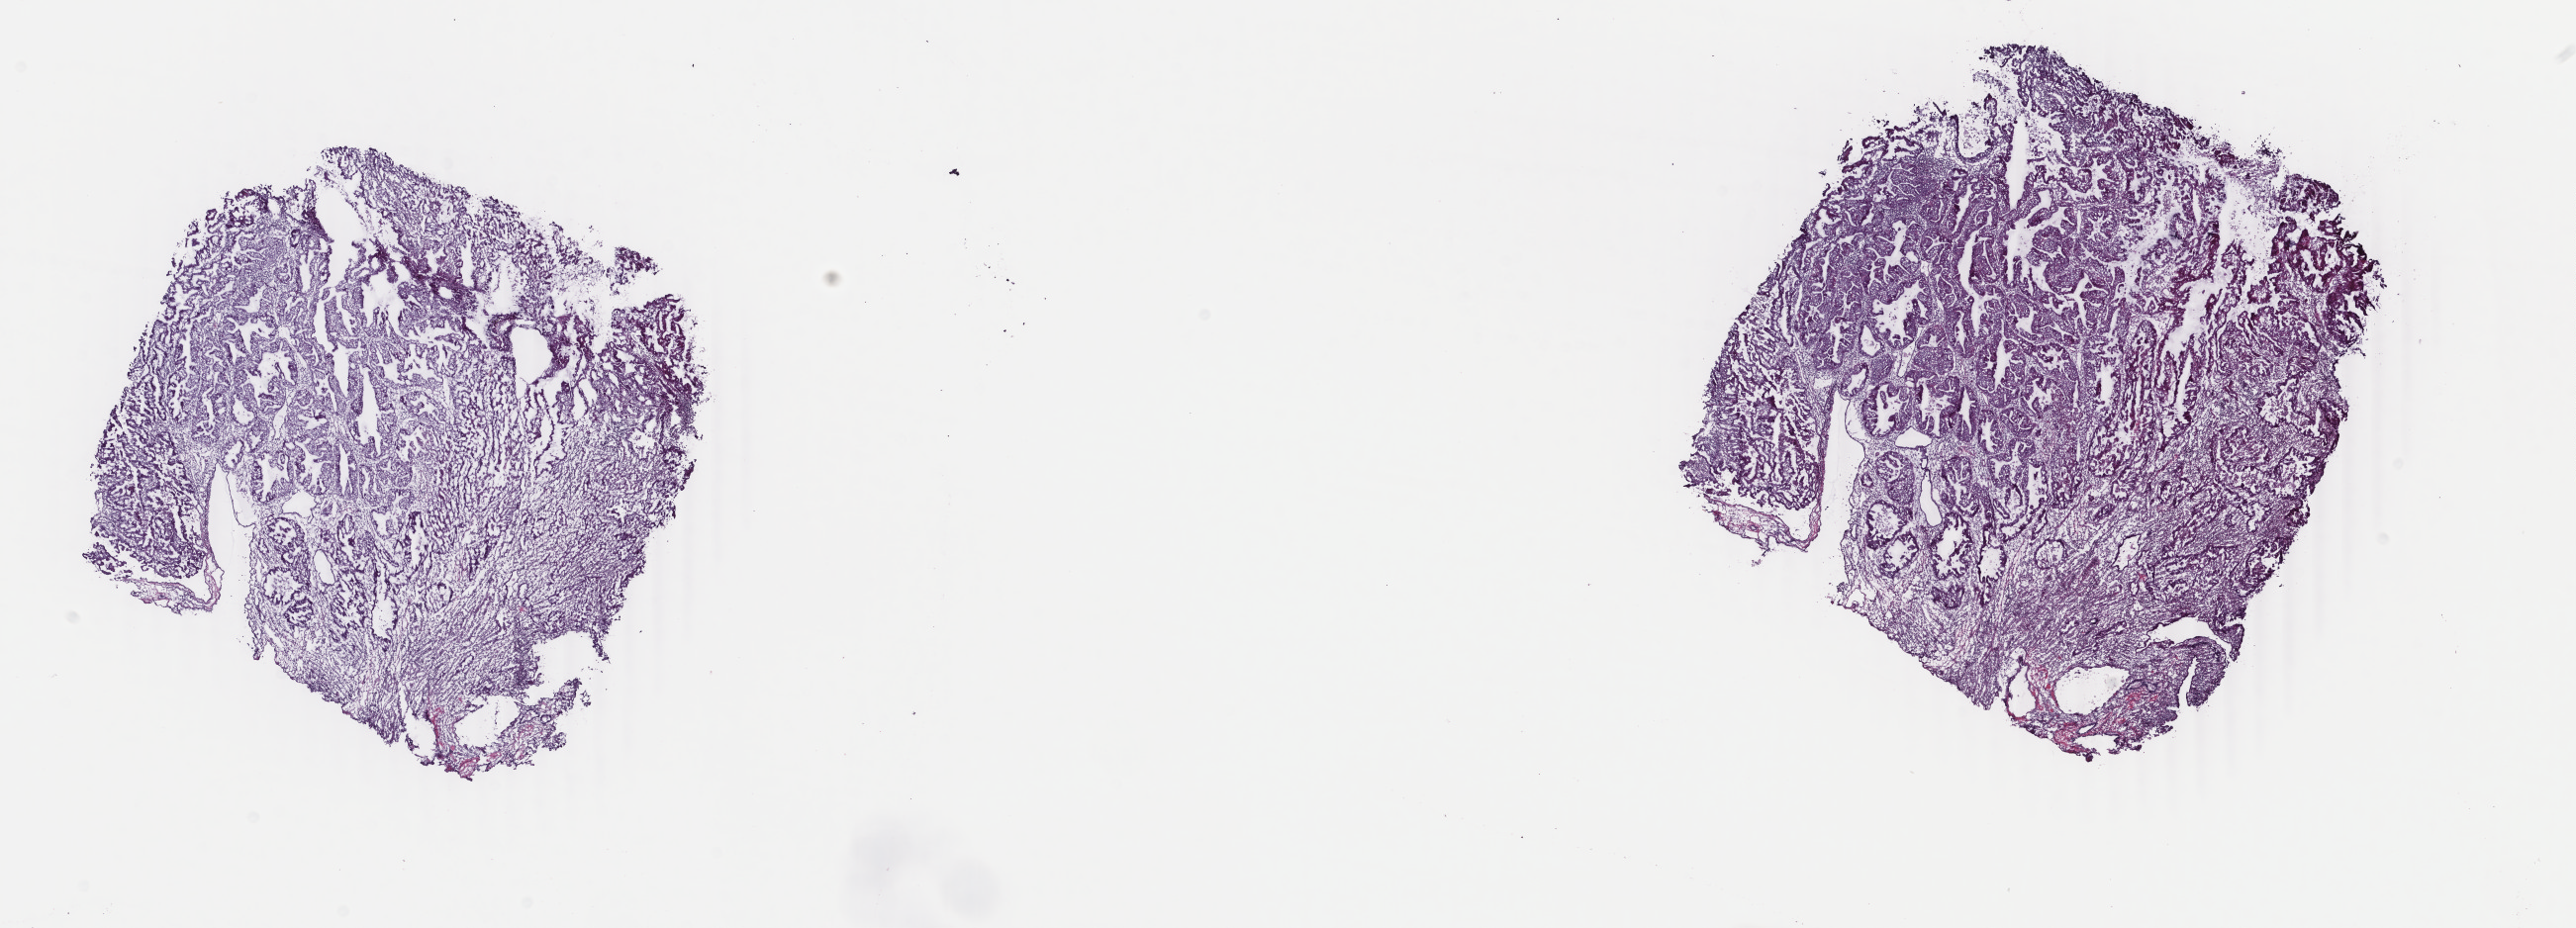
Hematoxylin and eosin (H&E) stained whole-slide image — low-resolution overview of the scanned area, about 20.7 x 7.5 mm, frozen section, sample: primary tumour, uterus. Patient: female, age at initial diagnosis 74 years. Histologic grade: high grade. Composition of this section per pathologist review: tumour cells 60%, tumour nuclei 60%, normal cells 0%, stromal cells 40%, necrosis 0%. Infiltration values recorded for this section: lymphocyte infiltration 10%, monocyte infiltration 0%, neutrophil infiltration 30%.
• lymph nodes positive (case pathology): 0 of 15 examined
• diagnosis: Serous cystadenocarcinoma, NOS (endometrium)
• FIGO stage: IV